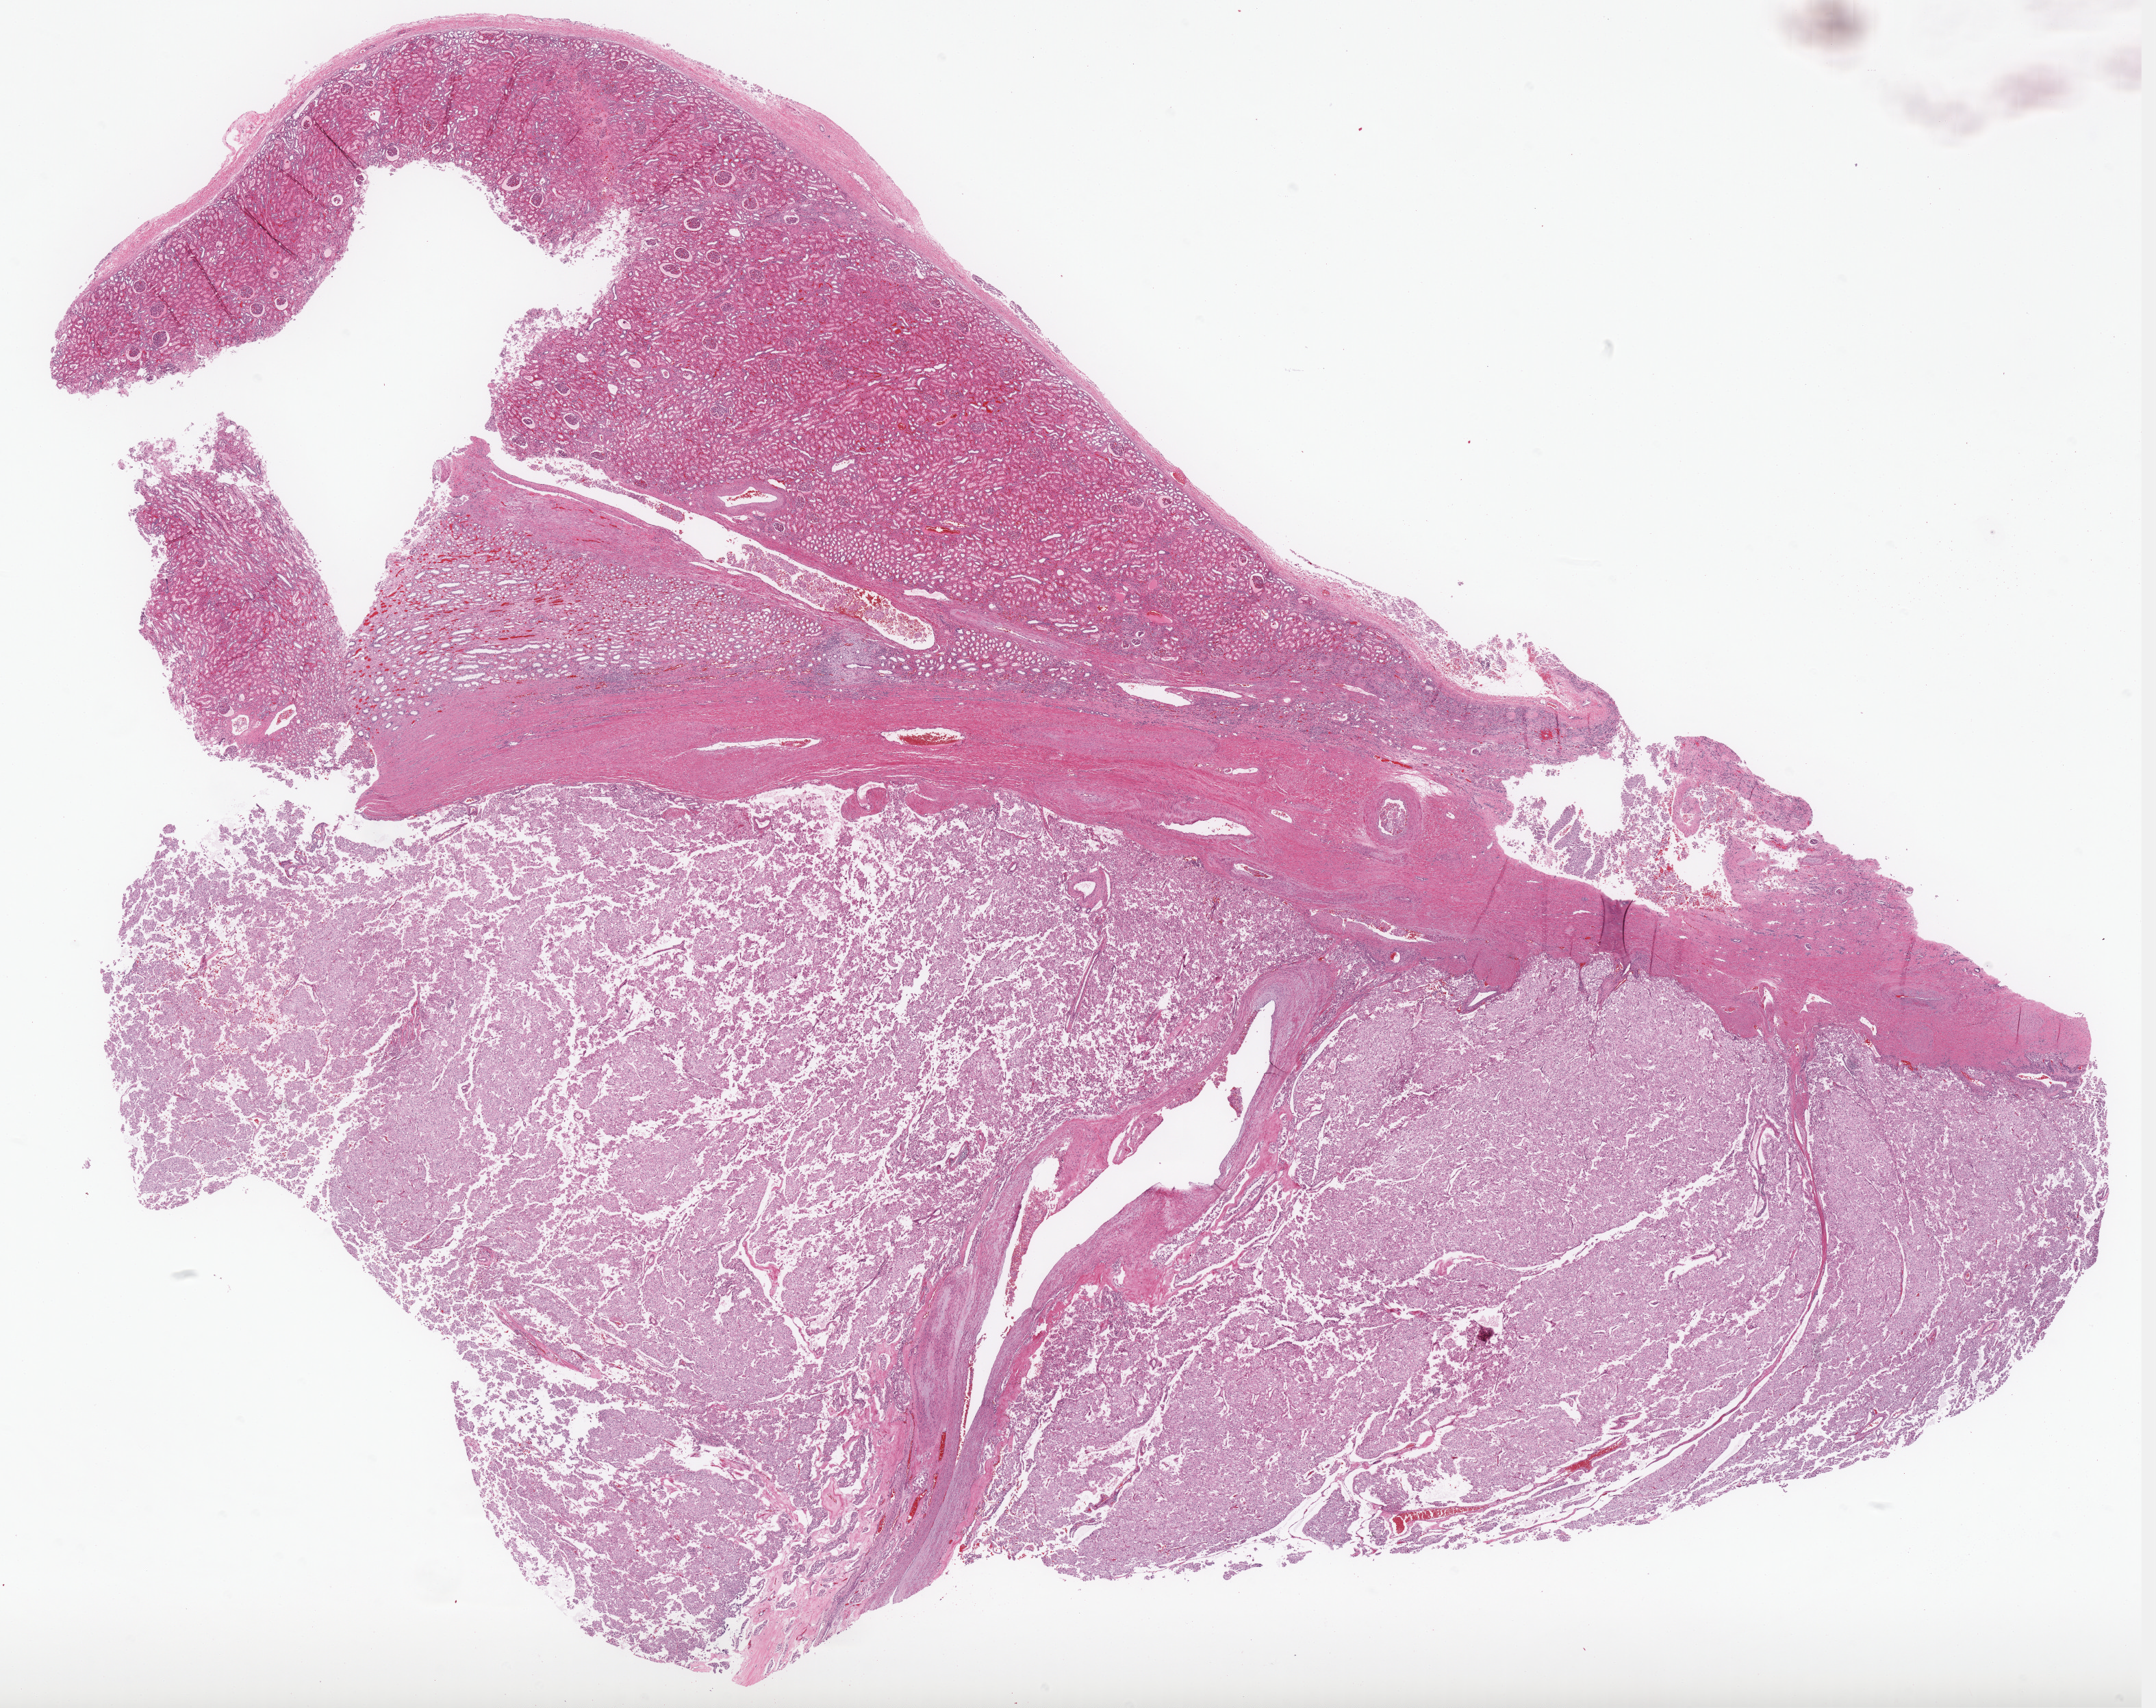
Digitized Hematoxylin and eosin (H&E) stained tissue section (whole slide), whole scanned area (about 25.2 x 19.9 mm) shown as a low-resolution overview, formalin-fixed paraffin-embedded (FFPE) diagnostic section, sample: primary tumour, kidney. Female, age 37 years at initial diagnosis.
- AJCC pathologic stage: III (6th edition)
- laterality: left
- TNM: T3a N0 M0
- pathologic diagnosis: Renal cell carcinoma, chromophobe type
- lymph nodes positive (case pathology): 0 of 6 examined